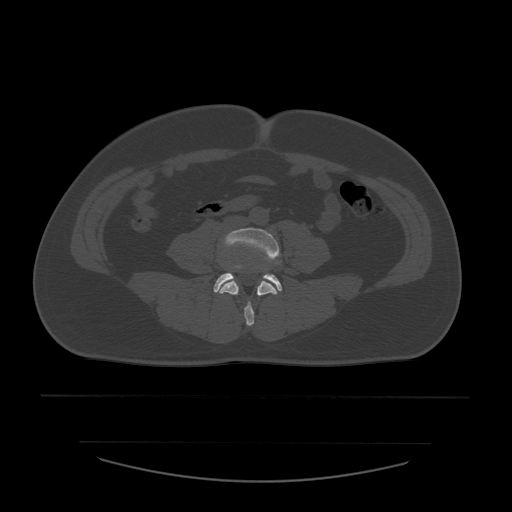
CT including the spine, one axial slice. Position 136 of 532 along the scan axis. Reconstruction kernel STANDARD. 120 kVp. Bone window (W 1800 / L 400 HU). 1.25 mm slice thickness. 512 × 512 image matrix, field of view 441 × 441 mm. Patient age 44 years. Case-level facts recorded for this patient, not image findings: primary cancer: soft tissue sarcoma.
Structures marked on this image (semi-automatically segmented with operator editing):
- L4 vertebra: bounding box [x1, y1, x2, y2] px = [218, 228, 282, 326]
- L5 vertebra: [214, 274, 282, 292]